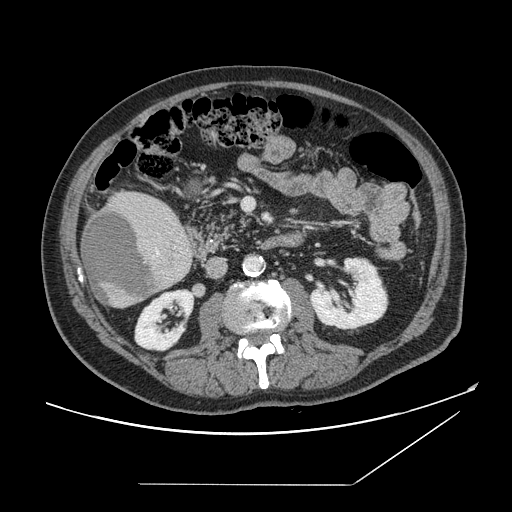
Contrast-enhanced abdominal CT, one axial slice; position 56 of 166 along the scan axis; intravenous contrast given; soft-tissue window (W 400 / L 40 HU); 512 × 512 image matrix, field of view 416 × 416 mm. Male patient, age 80 years. From the clinical record (not read from this slice): diagnosis: colorectal cancer liver metastases, imaged before liver resection; multiple liver metastases: no; largest metastasis: 2.2 cm; disease in both lobes: no.
Outlined on this slice (manually delineated by an expert):
- liver: bounding box <81,192,193,308> (left, top, right, bottom; pixels)
- planned liver remnant (the part of the liver to remain after resection): <147,197,158,202>
- liver metastasis: <83,209,157,304>